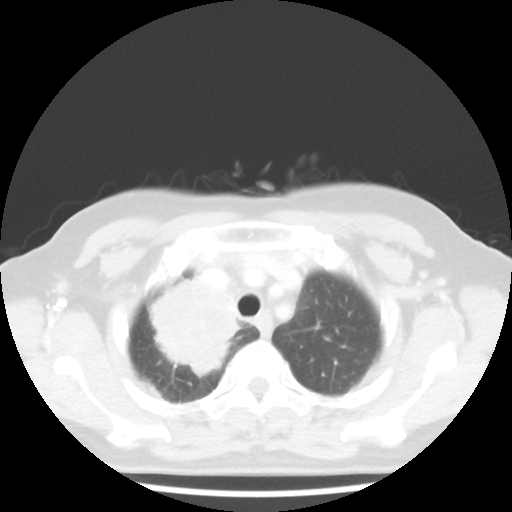
Chest CT, one axial slice; slice 37 of 44 in the series (ordered by position); 100 kVp; lung window (W 1500 / L -600 HU); 5 mm slice thickness; 512 × 512 image matrix. Female patient, age 62 years. Case-level facts recorded for this patient, not image findings: clinical TNM (as recorded): T3 N0 M0.
Structures marked on this image (rectangle marked by the reading radiologist):
- lung tumour (recorded histology: small cell carcinoma): bounding box (x1, y1, x2, y2) in pixels: (131, 275, 245, 376)